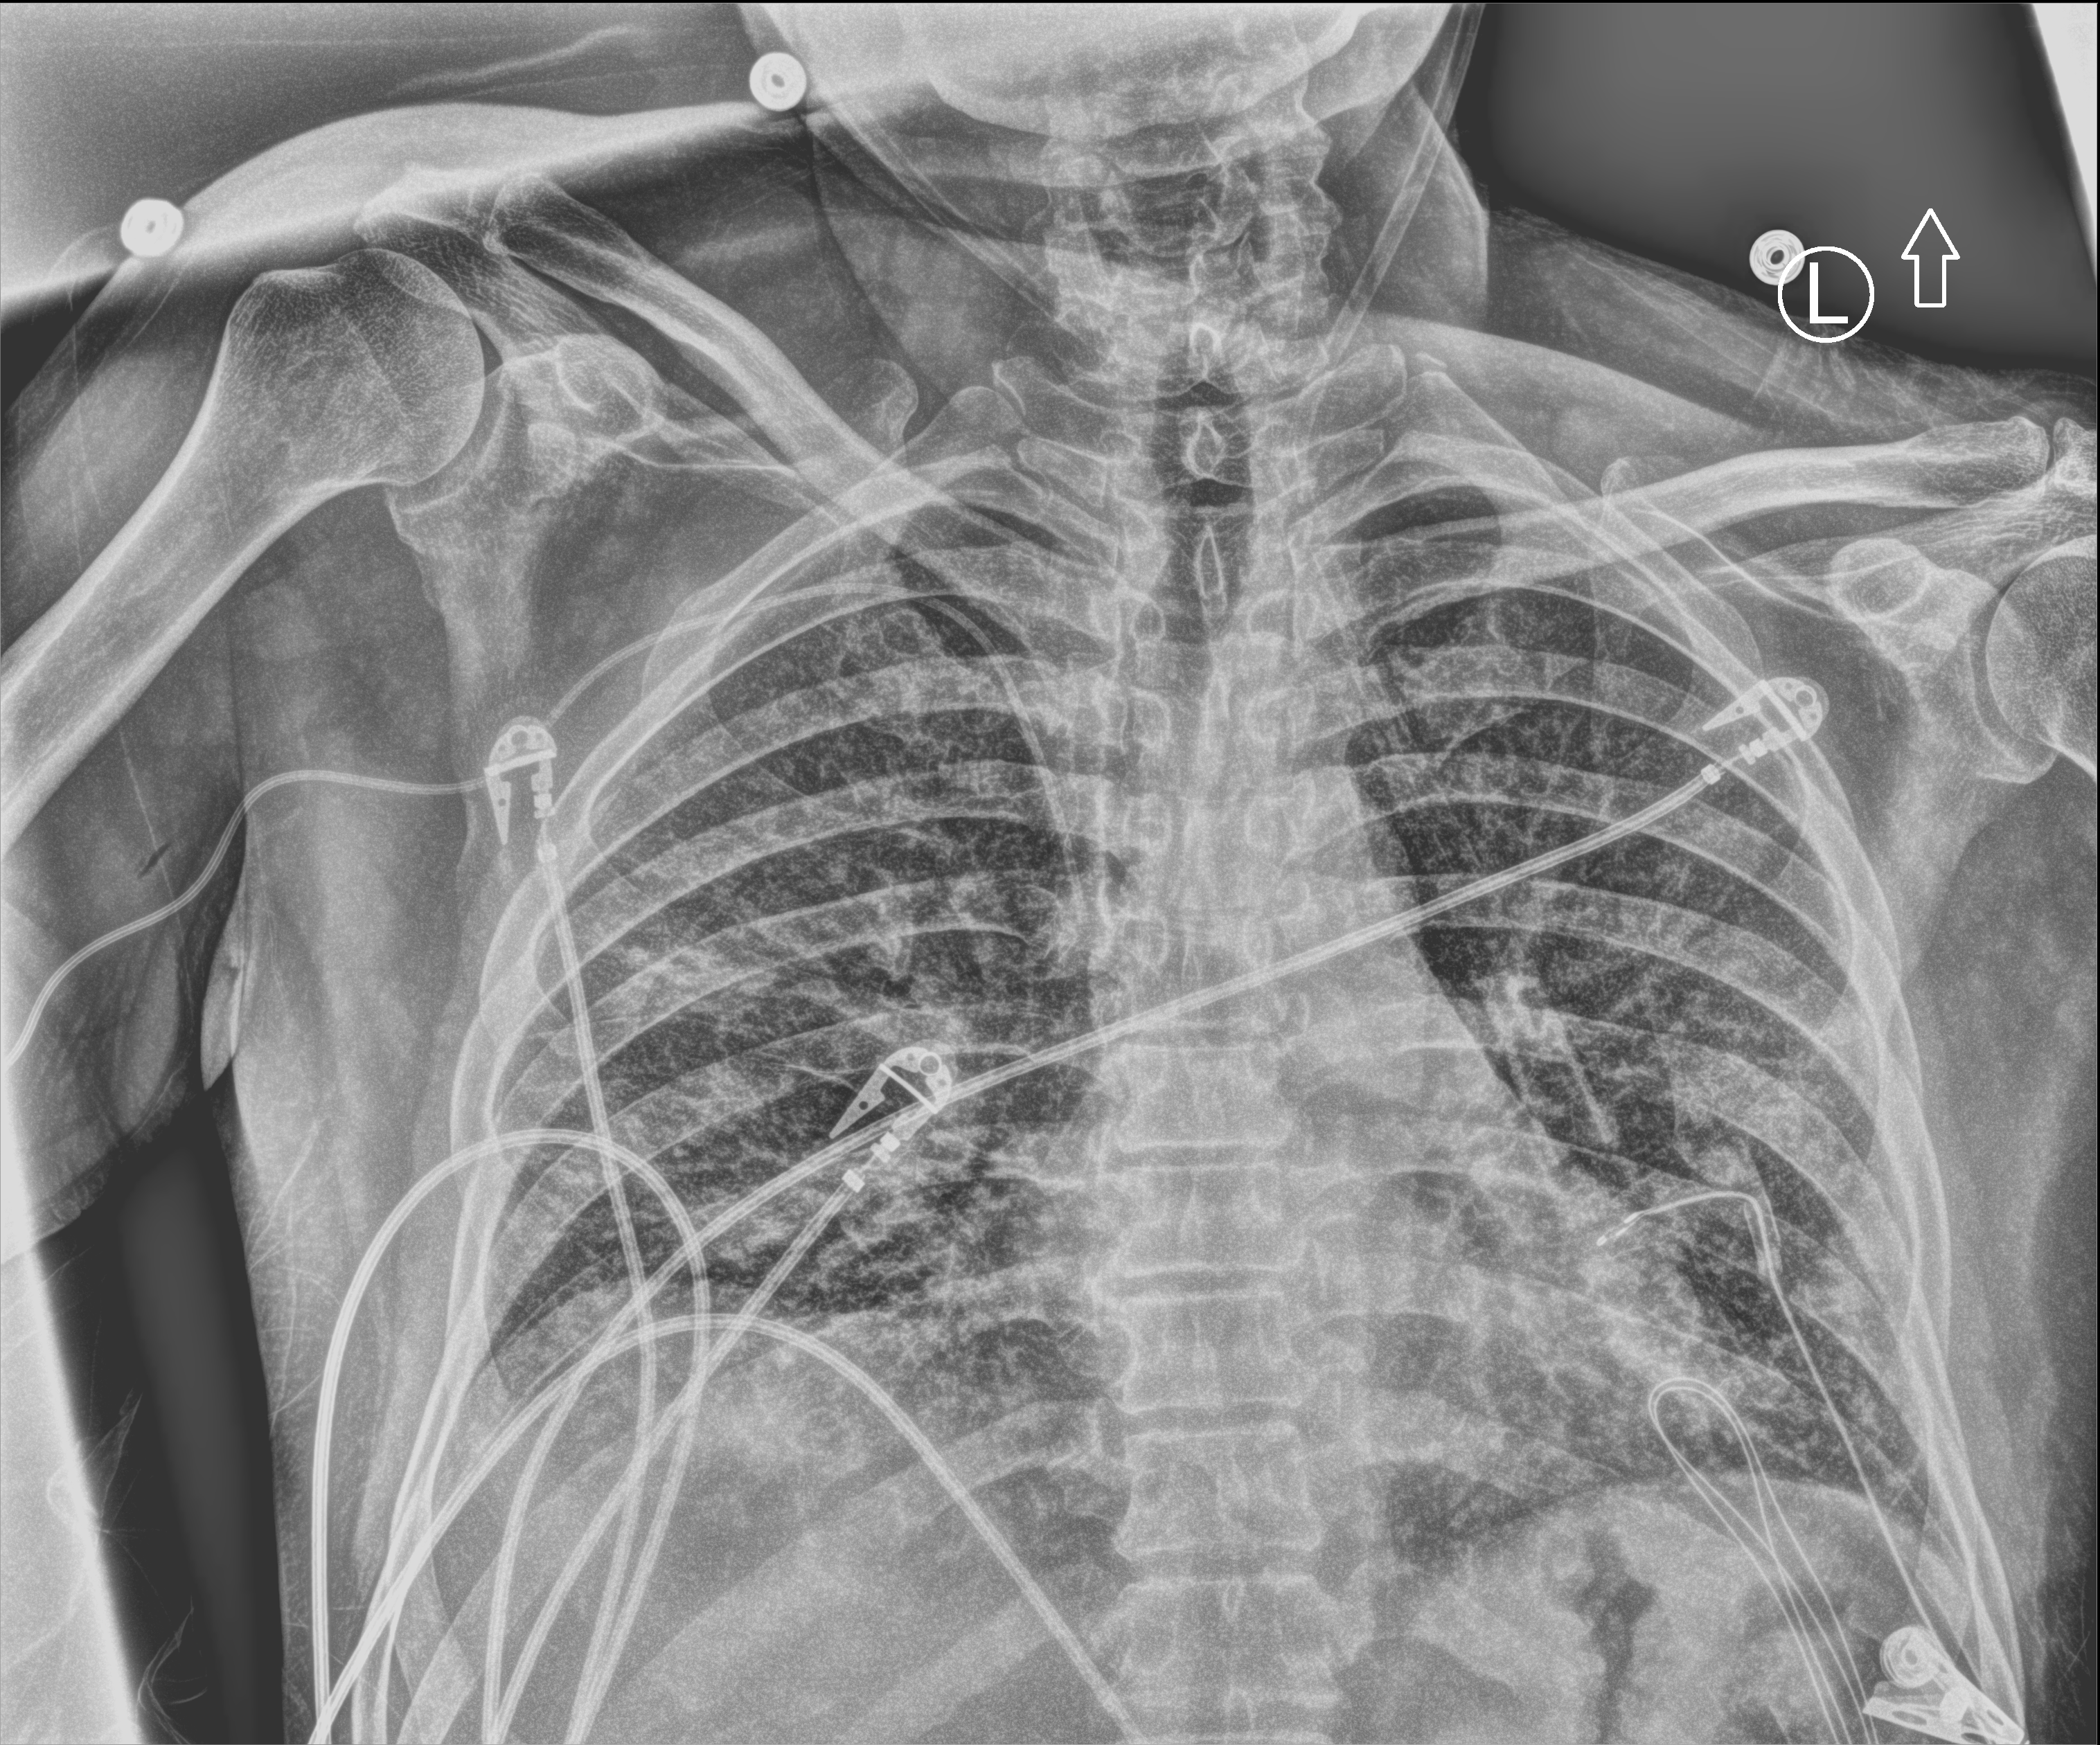
Portable chest radiograph, anteroposterior (AP) projection. Patient hospitalised with COVID-19; male, aged 18–59 years.
Admission-level facts for this patient (not findings on this image; timing relative to this image not recorded): admitted to intensive care during this hospital stay: yes; mechanically ventilated during this hospital stay: no; length of hospital stay: 38 days.